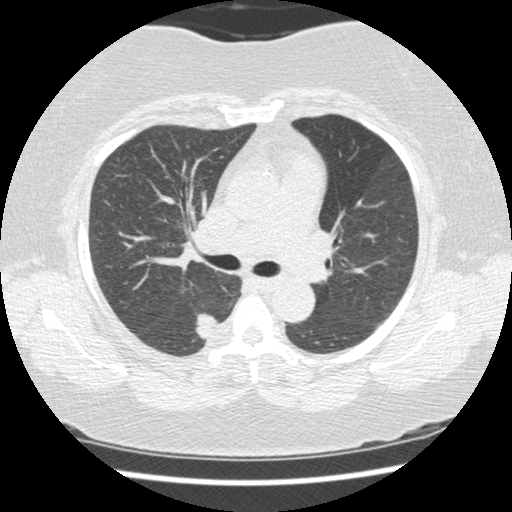
Chest CT (low-dose screening protocol), one axial image. Second annual screen. Lung window (W 1500 / L -600 HU). 1.25 mm slice thickness. Standard (soft-tissue) reconstruction kernel (STANDARD). Slice 68 of 210 in the series. Female, age 58 years at enrolment. Current smoker at enrolment.
- Lesion marked by an expert reader, box from (x=189, y=308) to (x=229, y=356) px.
- Screening reader's record for this exam (one nodule recorded; not confirmed to be the boxed lesion): non-calcified nodule or mass ≥4 mm, right lower lobe, 15 × 15 mm, spiculated (stellate) margins, soft tissue attenuation, pre-existing on the prior screen: yes; interval growth: yes.
- Later outcome: lung cancer diagnosed 21 days after this screen — adenocarcinoma, NOS, right lower lobe, stage IB (AJCC 6th edition), 15 mm at pathology.